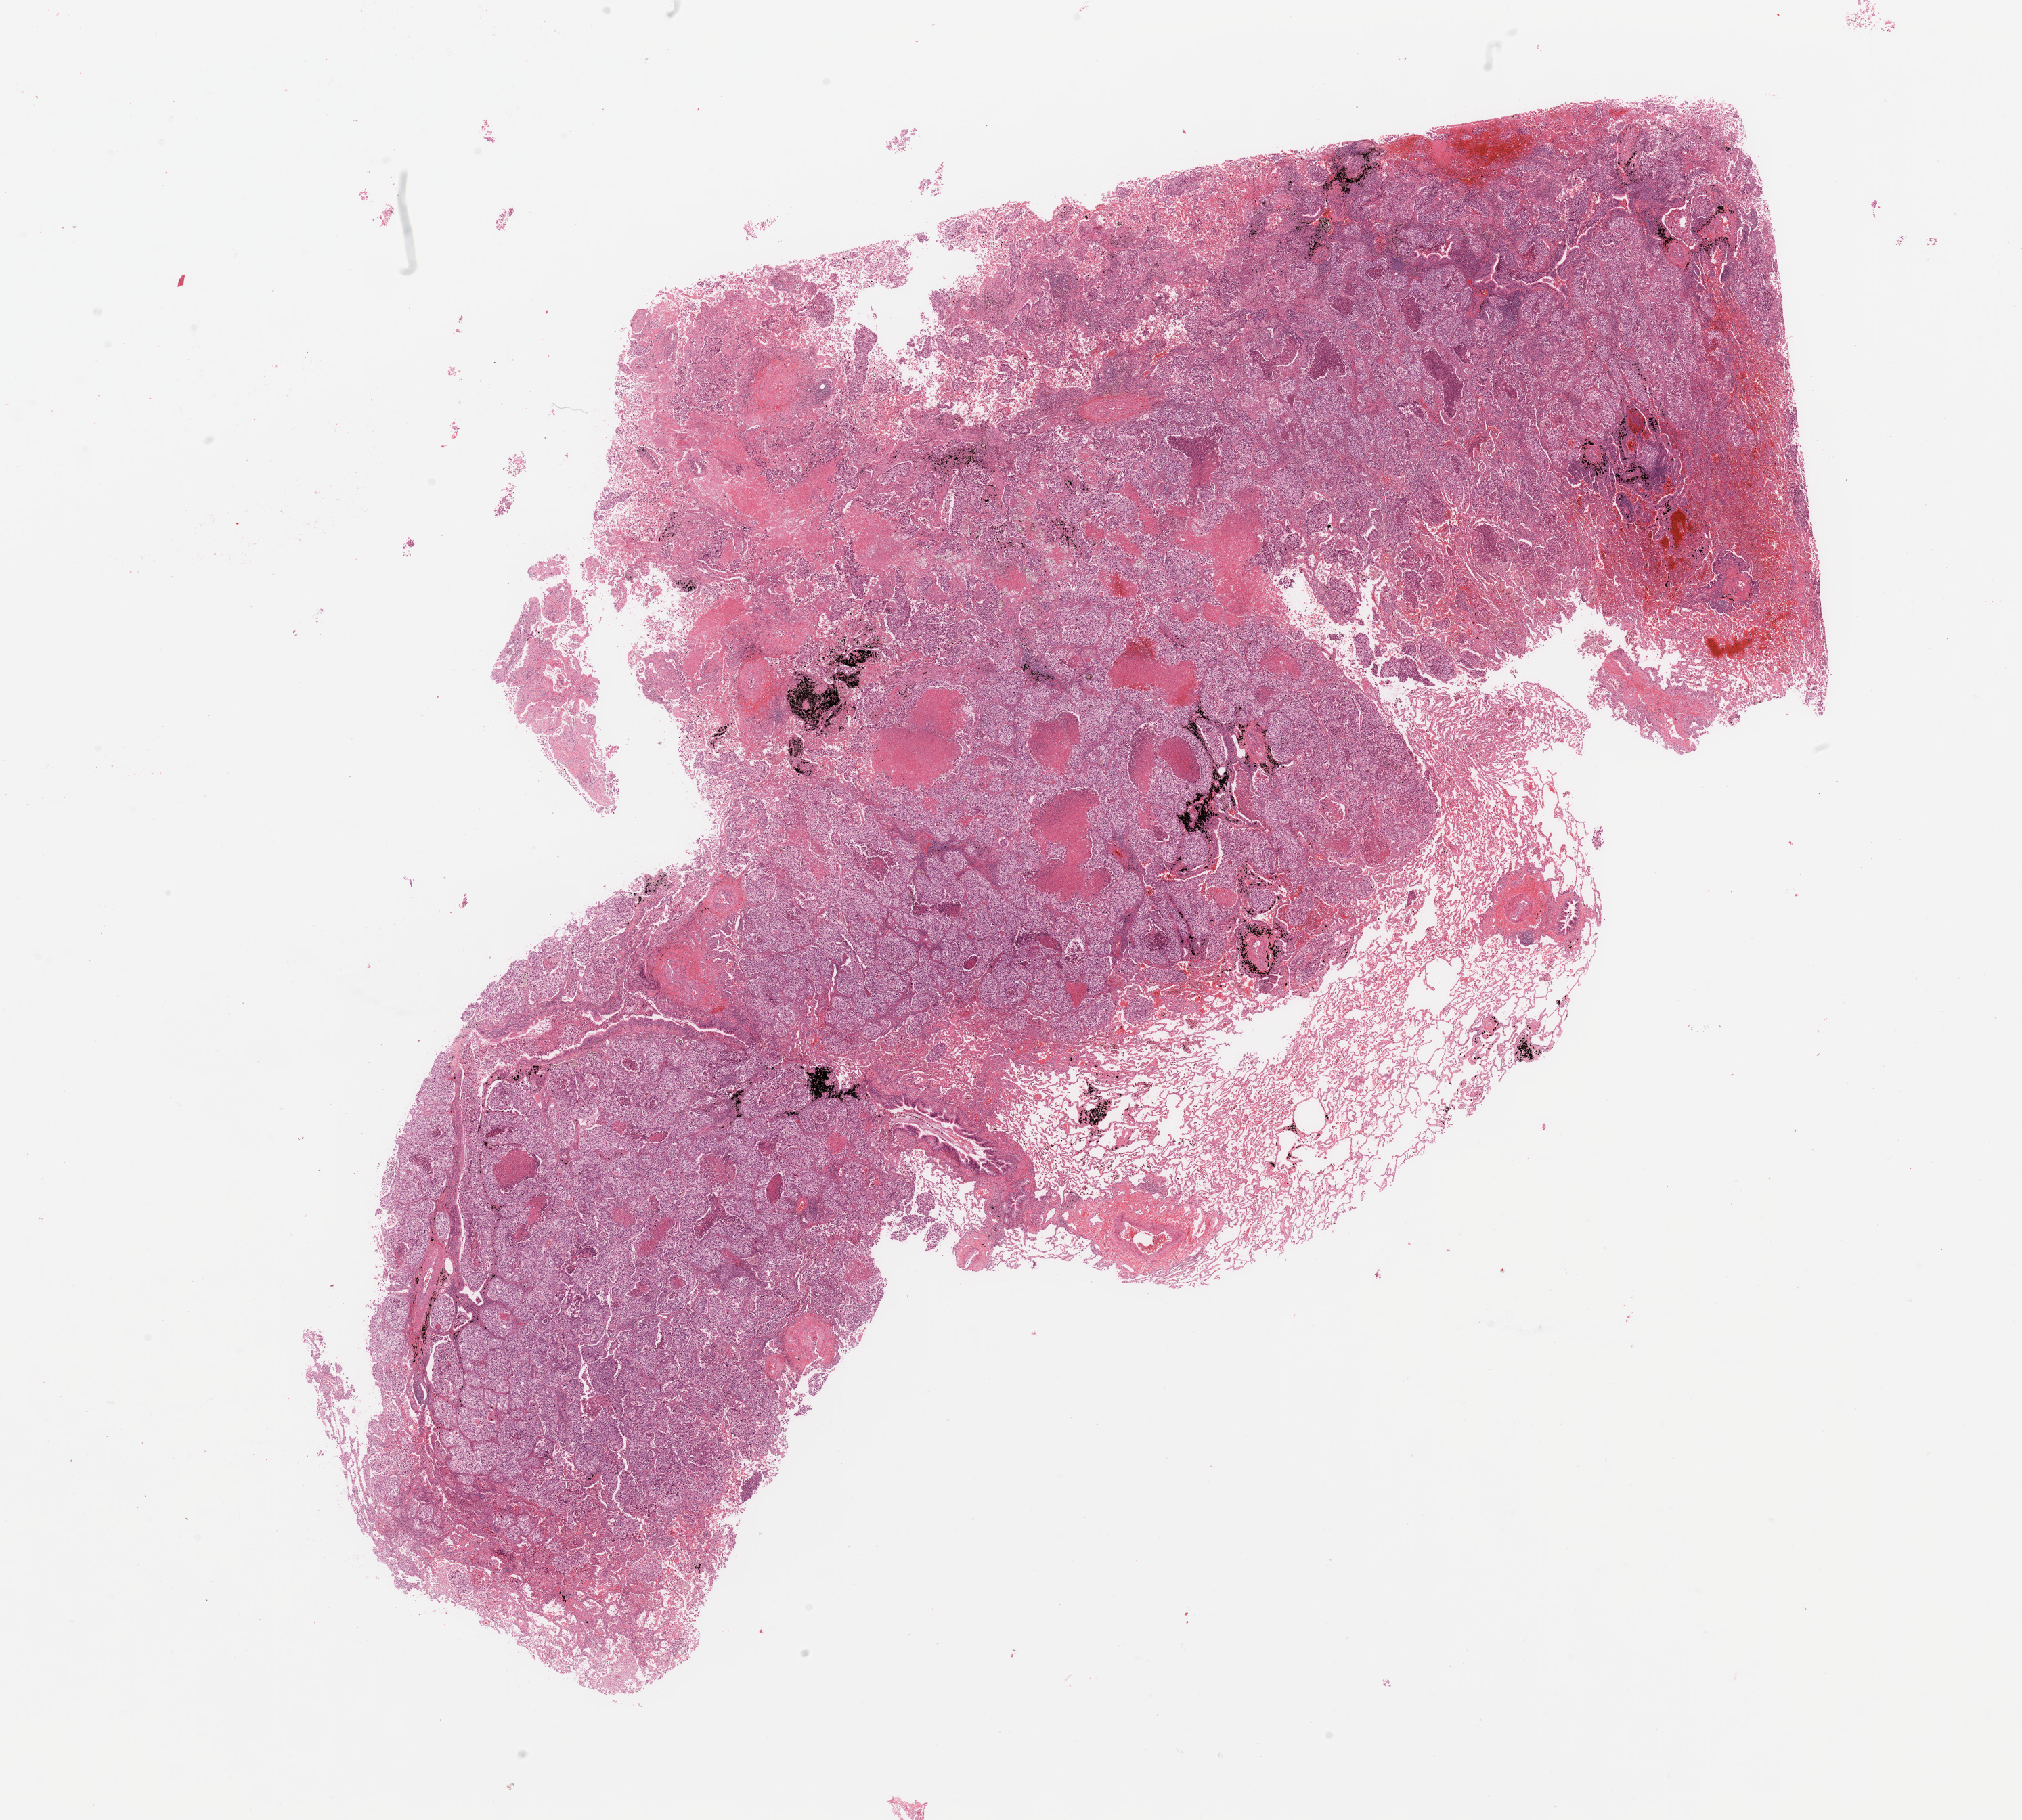
Whole-slide histology image, H&E, a low-resolution overview of the entire scanned area, about 23.6 x 21.3 mm (acquisition: 20x scan), tumour tissue sample, sampled site: lung. Patient: male, age 56 years. Histologic grade: G3 (poorly differentiated). Composition of this section per pathologist review: tumour nuclei 70%, necrosis 15%.
* histologic diagnosis: Adenocarcinoma, NOS
* primary tumour site (as recorded): left upper lobe
* AJCC pathologic stage: IB